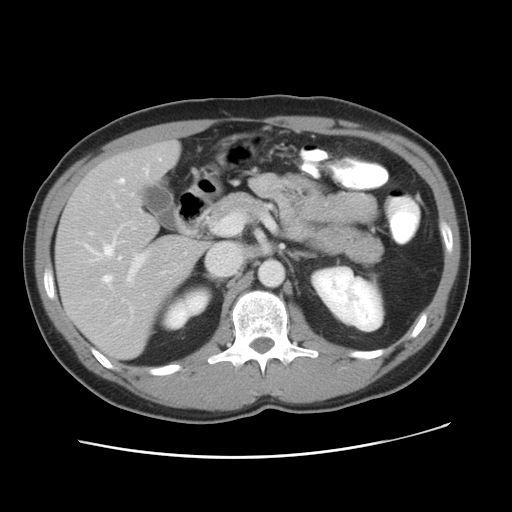
Contrast-enhanced abdominal CT, one axial slice; position 27 of 49 along the scan axis; soft-tissue window (W 400 / L 40 HU); 5 mm slice thickness; 512 × 512 image matrix, field of view 363 × 363 mm. Male patient, age 41 years. Case-level facts recorded for this patient, not image findings: diagnosis: colorectal cancer liver metastases, imaged before liver resection; multiple liver metastases: yes; largest metastasis: 0.7 cm; chemotherapy before resection: yes.
Annotated regions visible in this slice (manually delineated by an expert):
- hepatic veins: box from (x=86, y=157) to (x=238, y=288) px
- liver: (x=56, y=143)–(x=206, y=359)
- planned liver remnant (the part of the liver to remain after resection): (x=108, y=143)–(x=179, y=192)
- portal vein (with intrahepatic branches): (x=127, y=253)–(x=145, y=281)